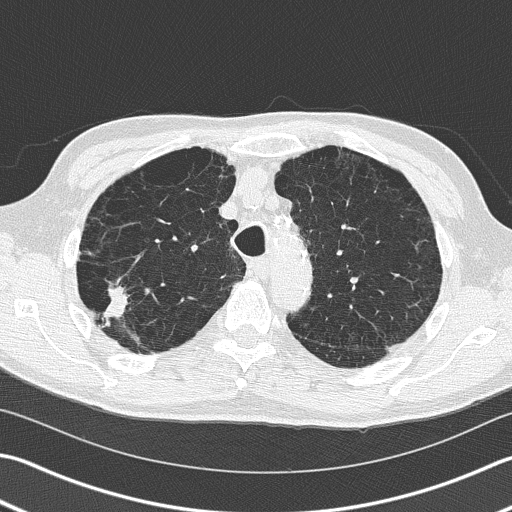
Low-dose screening chest CT, axial slice. First (baseline) screen. Lung window (W 1500 / L -600 HU). 2 mm slice thickness. Lung (sharp) reconstruction kernel (B50f). Slice 44 of 163 in the series. 512 × 512 image matrix, field of view 346 × 346 mm. Male participant, aged 66 years at enrolment. Current smoker at enrolment.
Expert-annotated lung lesion, bounding box (x1, y1, x2, y2) in pixels: (78, 261, 142, 339). Reader record for this screening exam (exam-level; its link to the box is not recorded): non-calcified nodule or mass ≥4 mm, right upper lobe, 39 × 23 mm, spiculated (stellate) margins, soft tissue attenuation. Later outcome: lung cancer diagnosed 36 days after this screen — squamous cell carcinoma, NOS, right upper lobe, poorly differentiated (G3), stage IB (AJCC 6th edition), 23 mm at pathology.